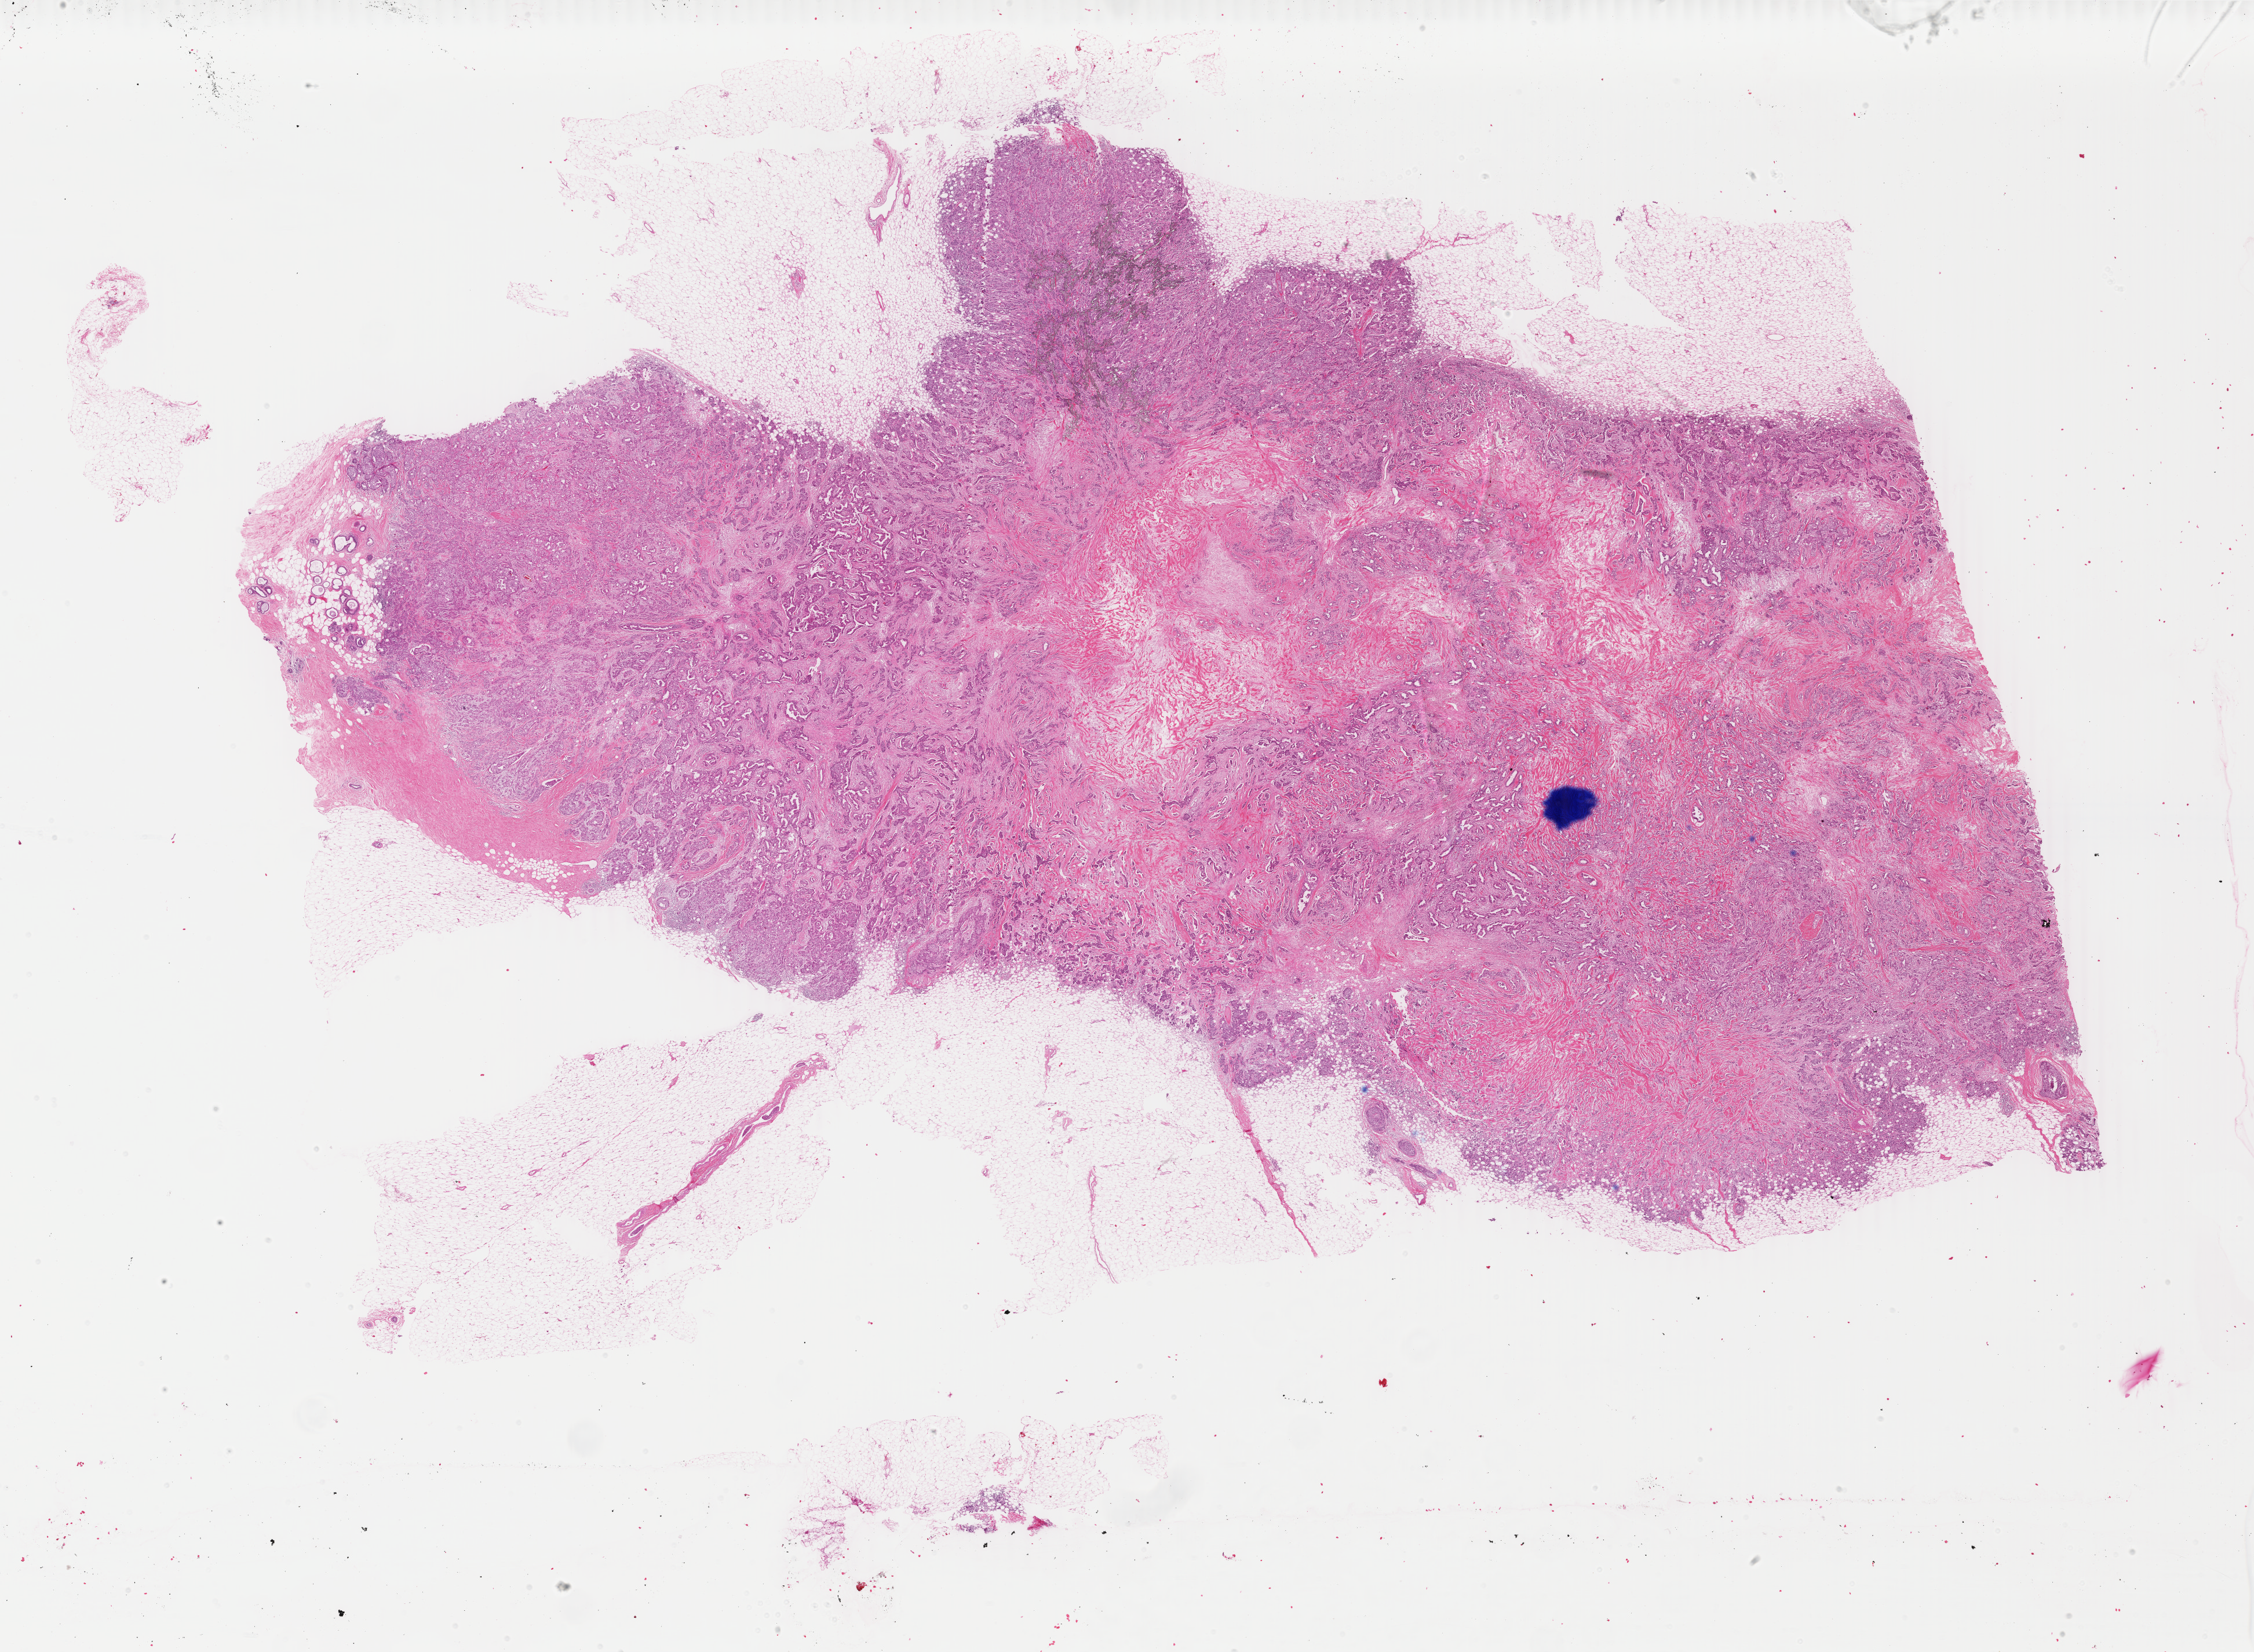
H&E-stained whole-slide image — whole scanned area (about 30.9 x 22.7 mm, from a 40x scan) shown as a low-resolution overview; FFPE section; primary tumour sample from the breast. Female patient; age at initial diagnosis 67 years.
Laterality: right. AJCC pathologic stage: IIB. Lymph nodes positive (case pathology): 4 of 7 examined. TNM: T2 N1b M0. Pathologic diagnosis: Infiltrating duct carcinoma, NOS.